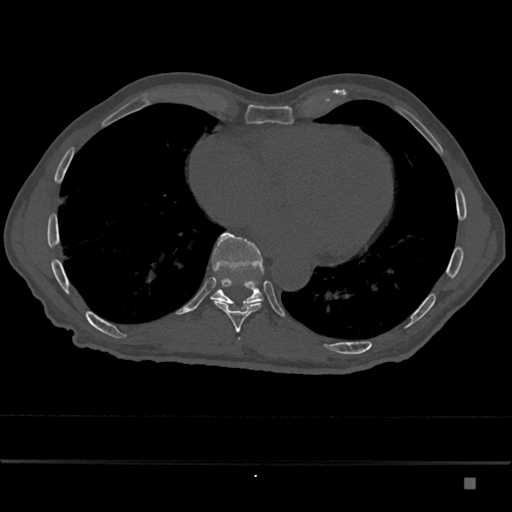
CT including the spine, one axial slice; position 780 of 797 along the scan axis; bone window (W 1800 / L 400 HU); 0.5 mm slice thickness; 512 × 512 image matrix. Patient: male, 72 years. Case-level facts recorded for this patient, not image findings: primary cancer: prostate.
Outlined on this slice (semi-automatically segmented with operator editing):
- T10 vertebra: bounding box <210,232,264,307> (left, top, right, bottom; pixels)
- T9 vertebra: <213,300,263,333>